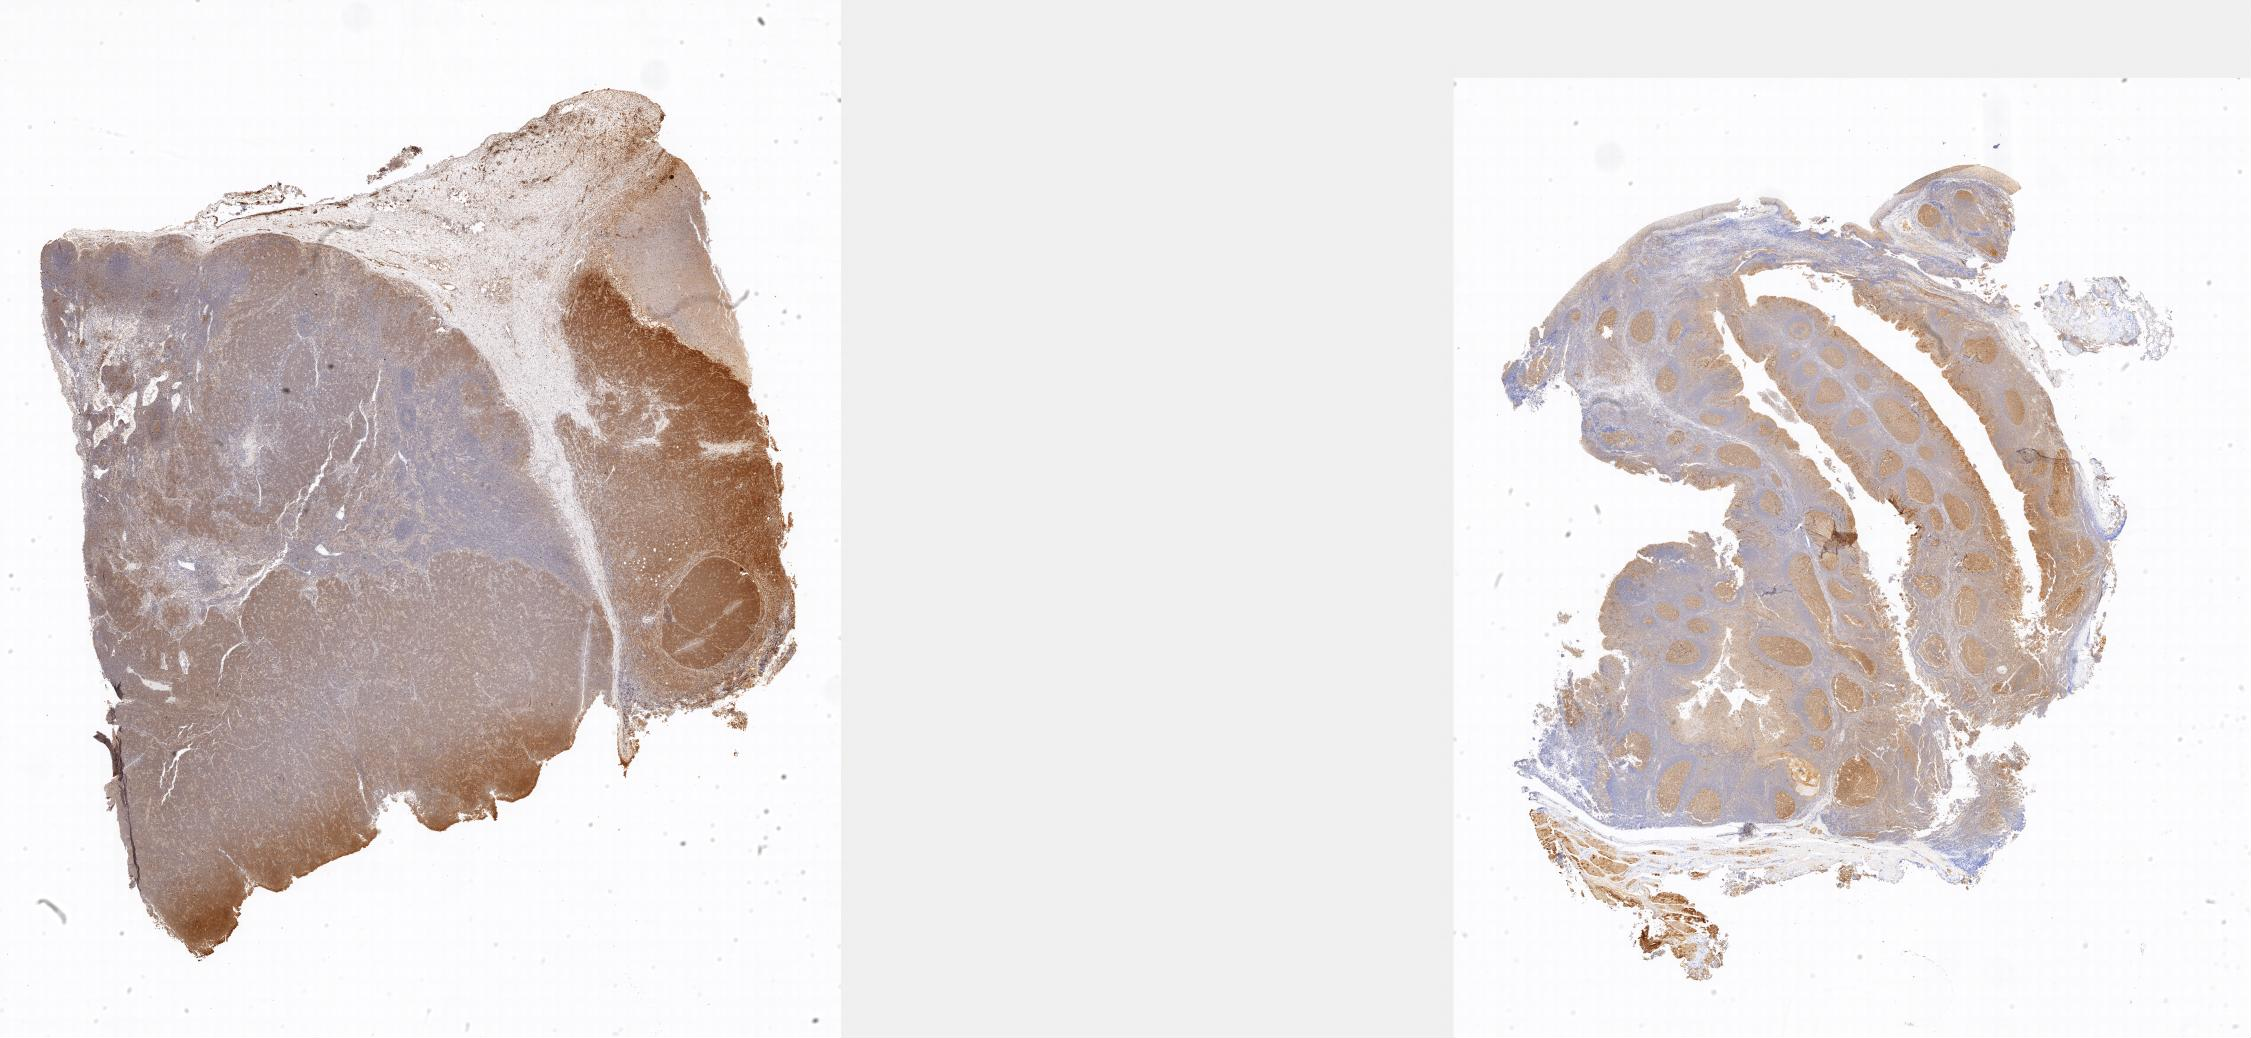
Whole-slide image, immunohistochemical stain for BCL6, low-resolution overview of the scanned area; tumor tissue; anatomic site: abdominal lymph node. Female patient, aged 14.
* diagnosis: Burkitt lymphoma, NOS